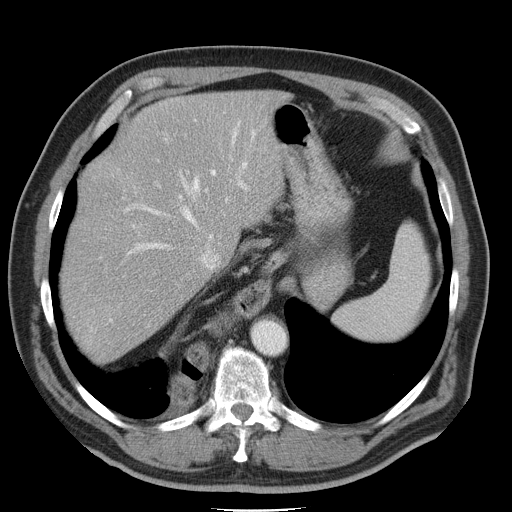
Contrast-enhanced abdominal CT, one axial slice. Position 36 of 45 along the scan axis. Intravenous contrast given. Soft-tissue window (W 400 / L 40 HU). 5 mm slice thickness. 512 × 512 image matrix, field of view 386 × 386 mm. Male patient, age 65 years. From the clinical record (not read from this slice): diagnosis: colorectal cancer liver metastases, imaged before liver resection; multiple liver metastases: yes.
Annotated regions visible in this slice (outlined manually by an expert reader):
- hepatic veins: bounding box [x1, y1, x2, y2] px = [83, 120, 251, 337]
- liver: [64, 91, 280, 356]
- planned liver remnant (the part of the liver to remain after resection): [107, 91, 279, 255]
- portal vein (with intrahepatic branches): [130, 169, 216, 237]